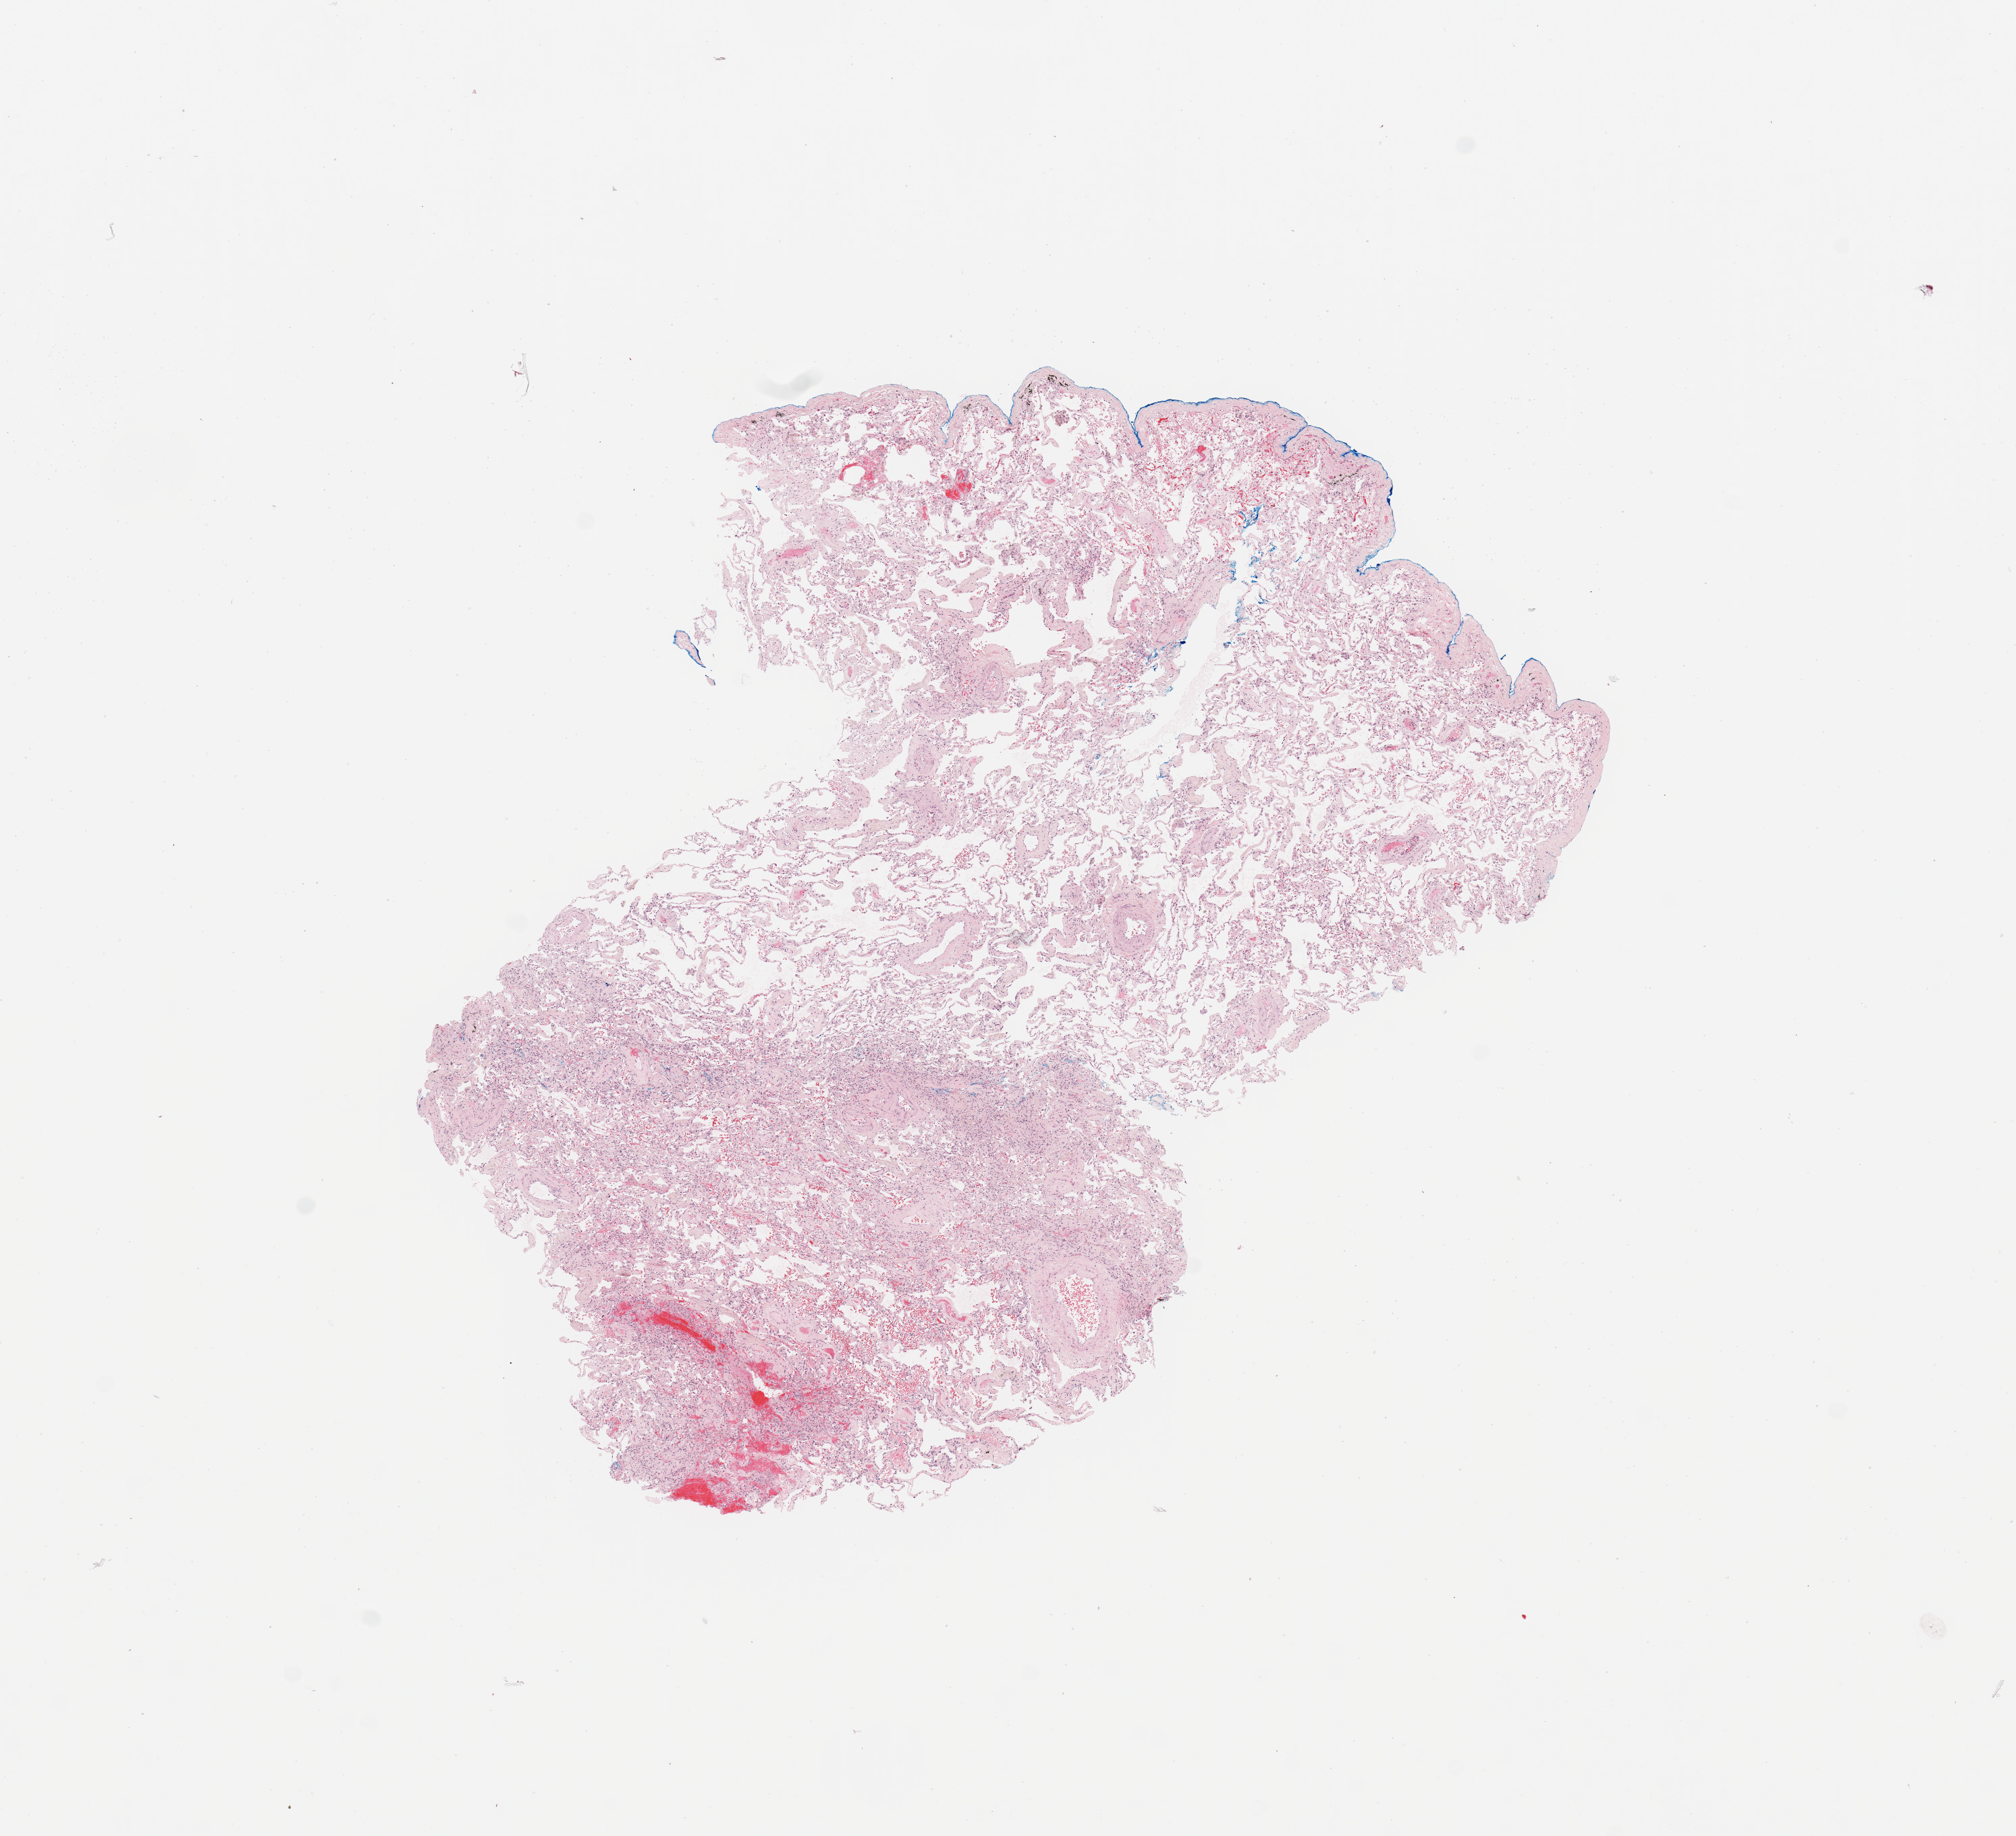
Hematoxylin and eosin (H&E) stained whole-slide image — low-resolution overview of the scanned area, about 11.8 x 10.8 mm (from a 20x scan). Normal (non-tumour) tissue sample, sampled site: lung. Male, 71 y/o.
This section: normal (non-tumour) tissue from the same patient. Patient diagnosis: Adenocarcinoma, NOS.